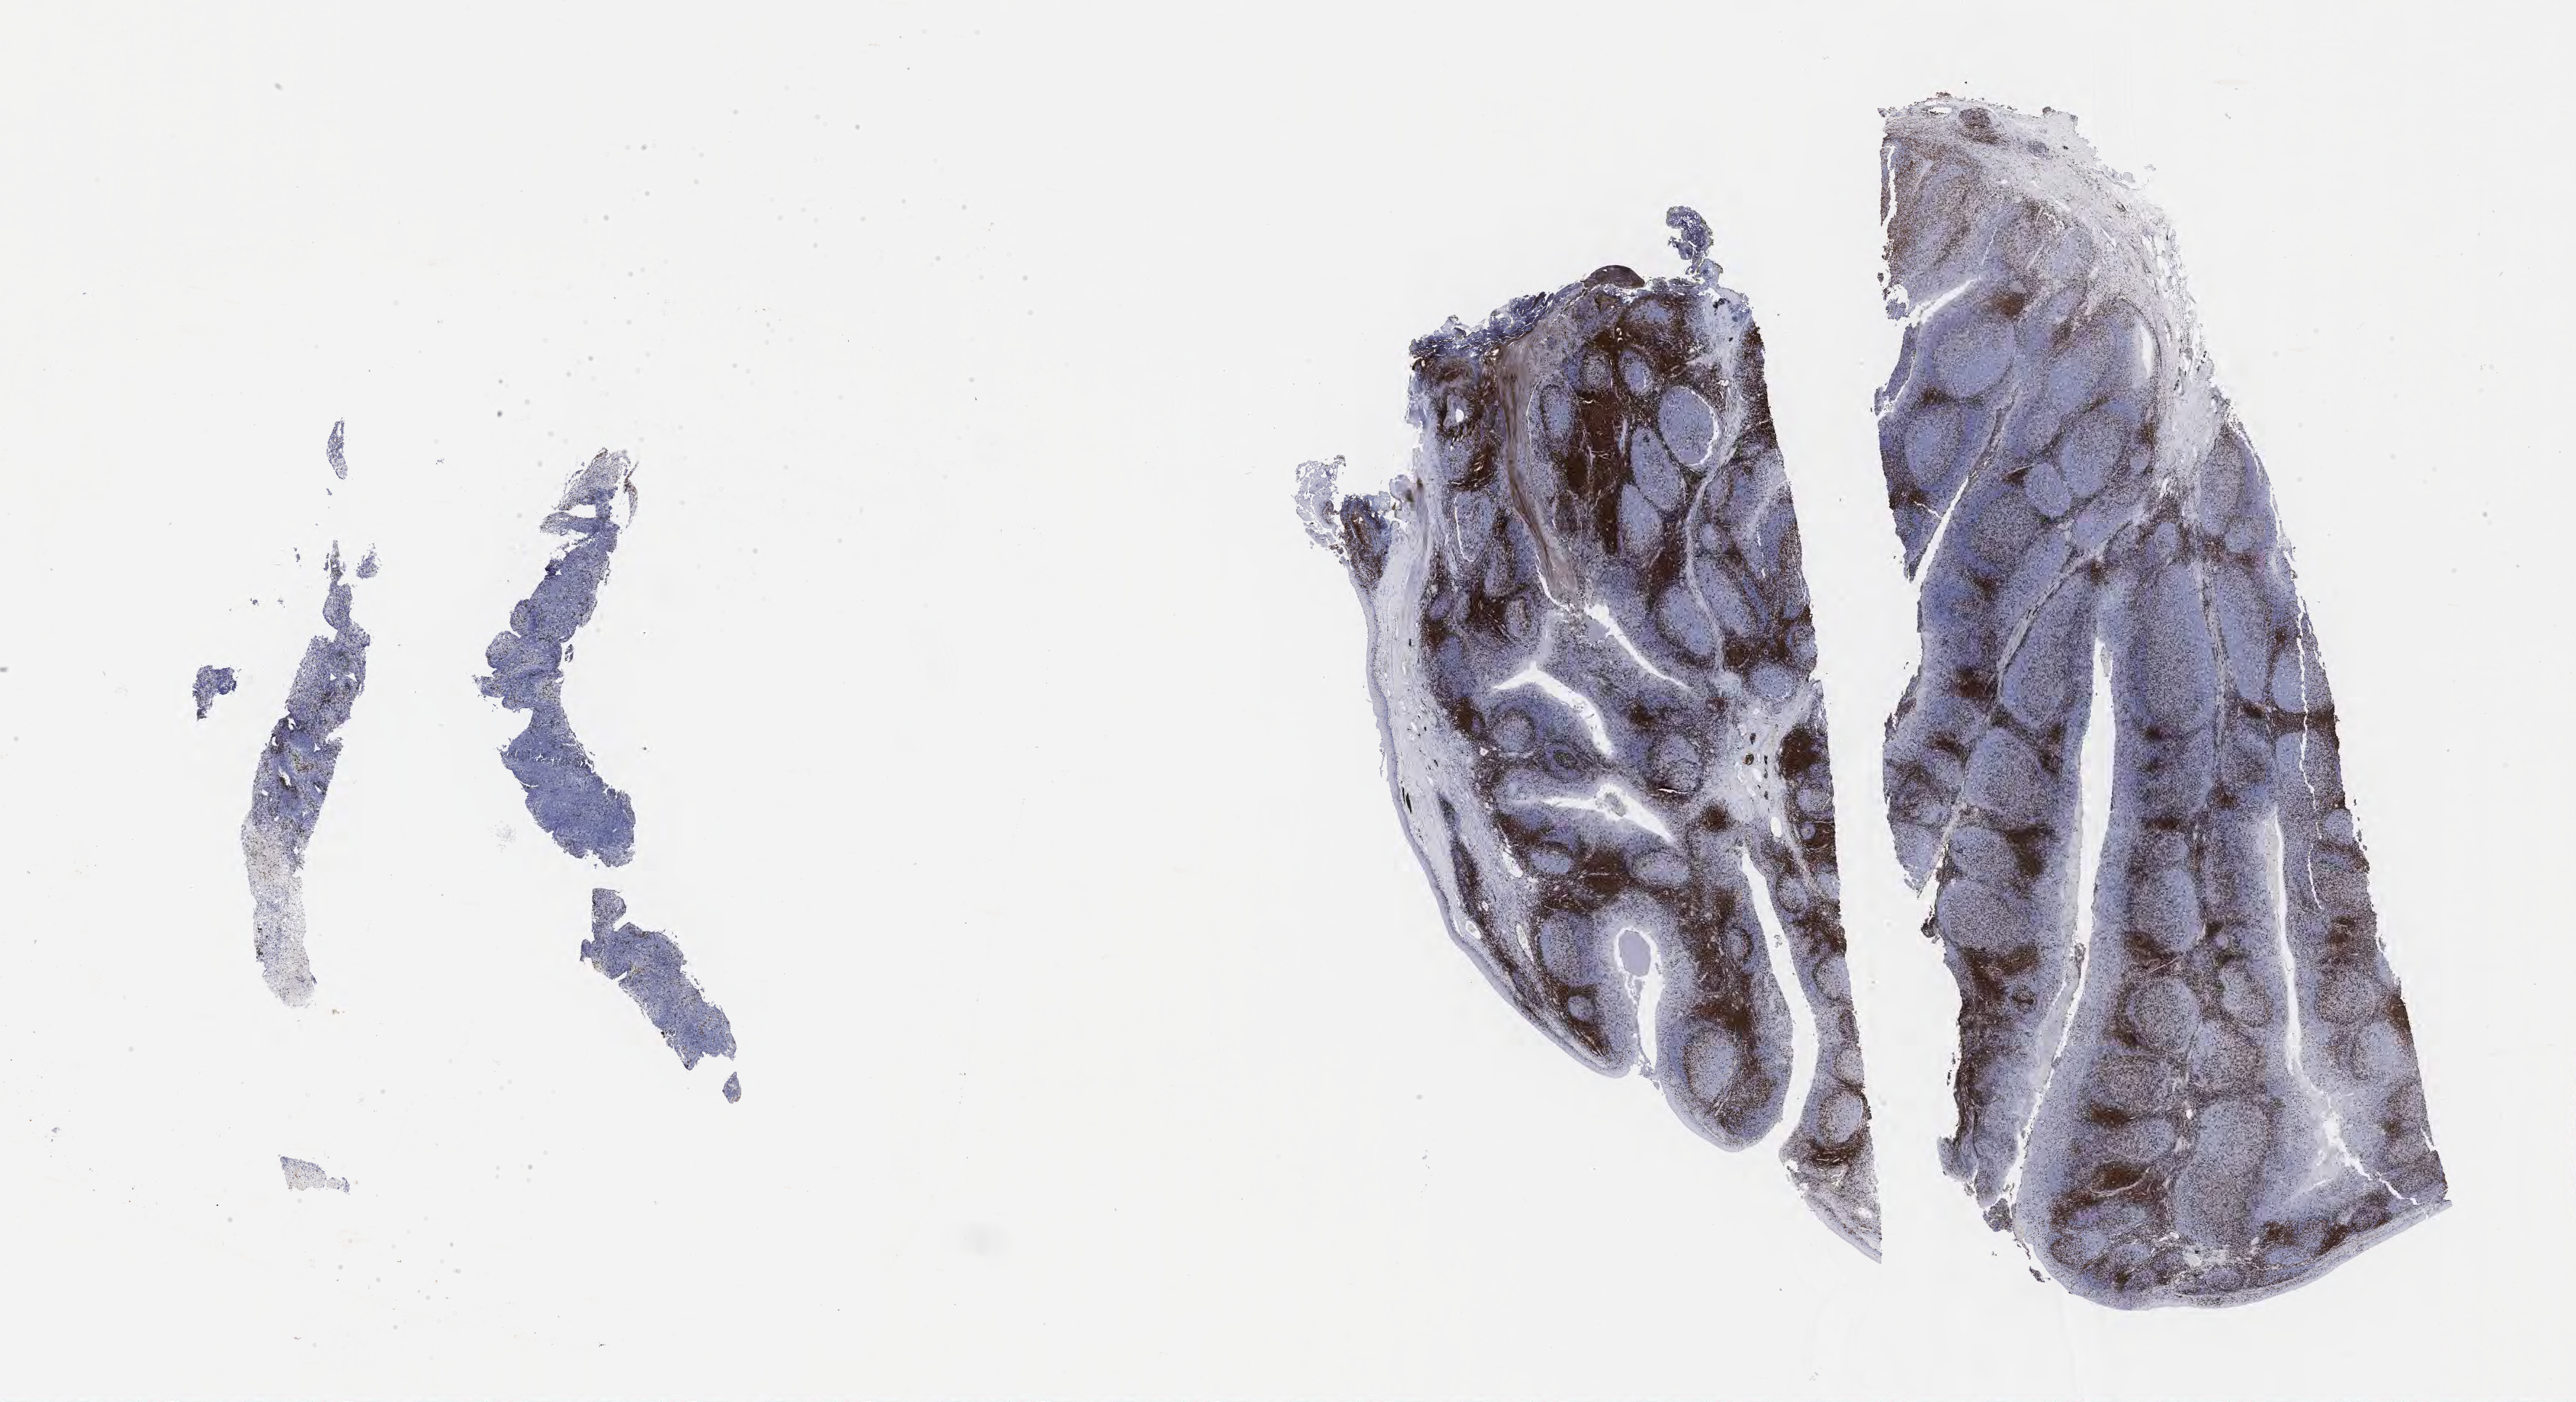
Immunohistochemistry (IHC) whole-slide image stained for CD3, whole scanned area (about 28.7 x 15.6 mm) shown as a low-resolution overview, specimen: tumor tissue. Female patient, aged 12.
- diagnosis: Burkitt lymphoma, NOS